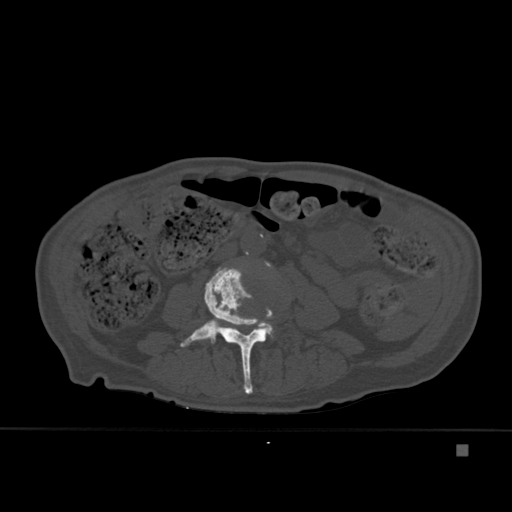
CT including the spine, one axial slice. Slice 139 of 451 in the series (ordered by position). Bone window (W 1800 / L 400 HU). 512 × 512 image matrix, field of view 378 × 378 mm. Patient: male, 75 years. From the clinical record (not read from this slice): primary cancer: prostate.
Annotated regions visible in this slice (semi-automatic segmentation, software-assisted and operator-edited):
- L3 vertebra: bounding box [x1, y1, x2, y2] px = [180, 267, 273, 394]
- L4 vertebra: [231, 261, 274, 339]